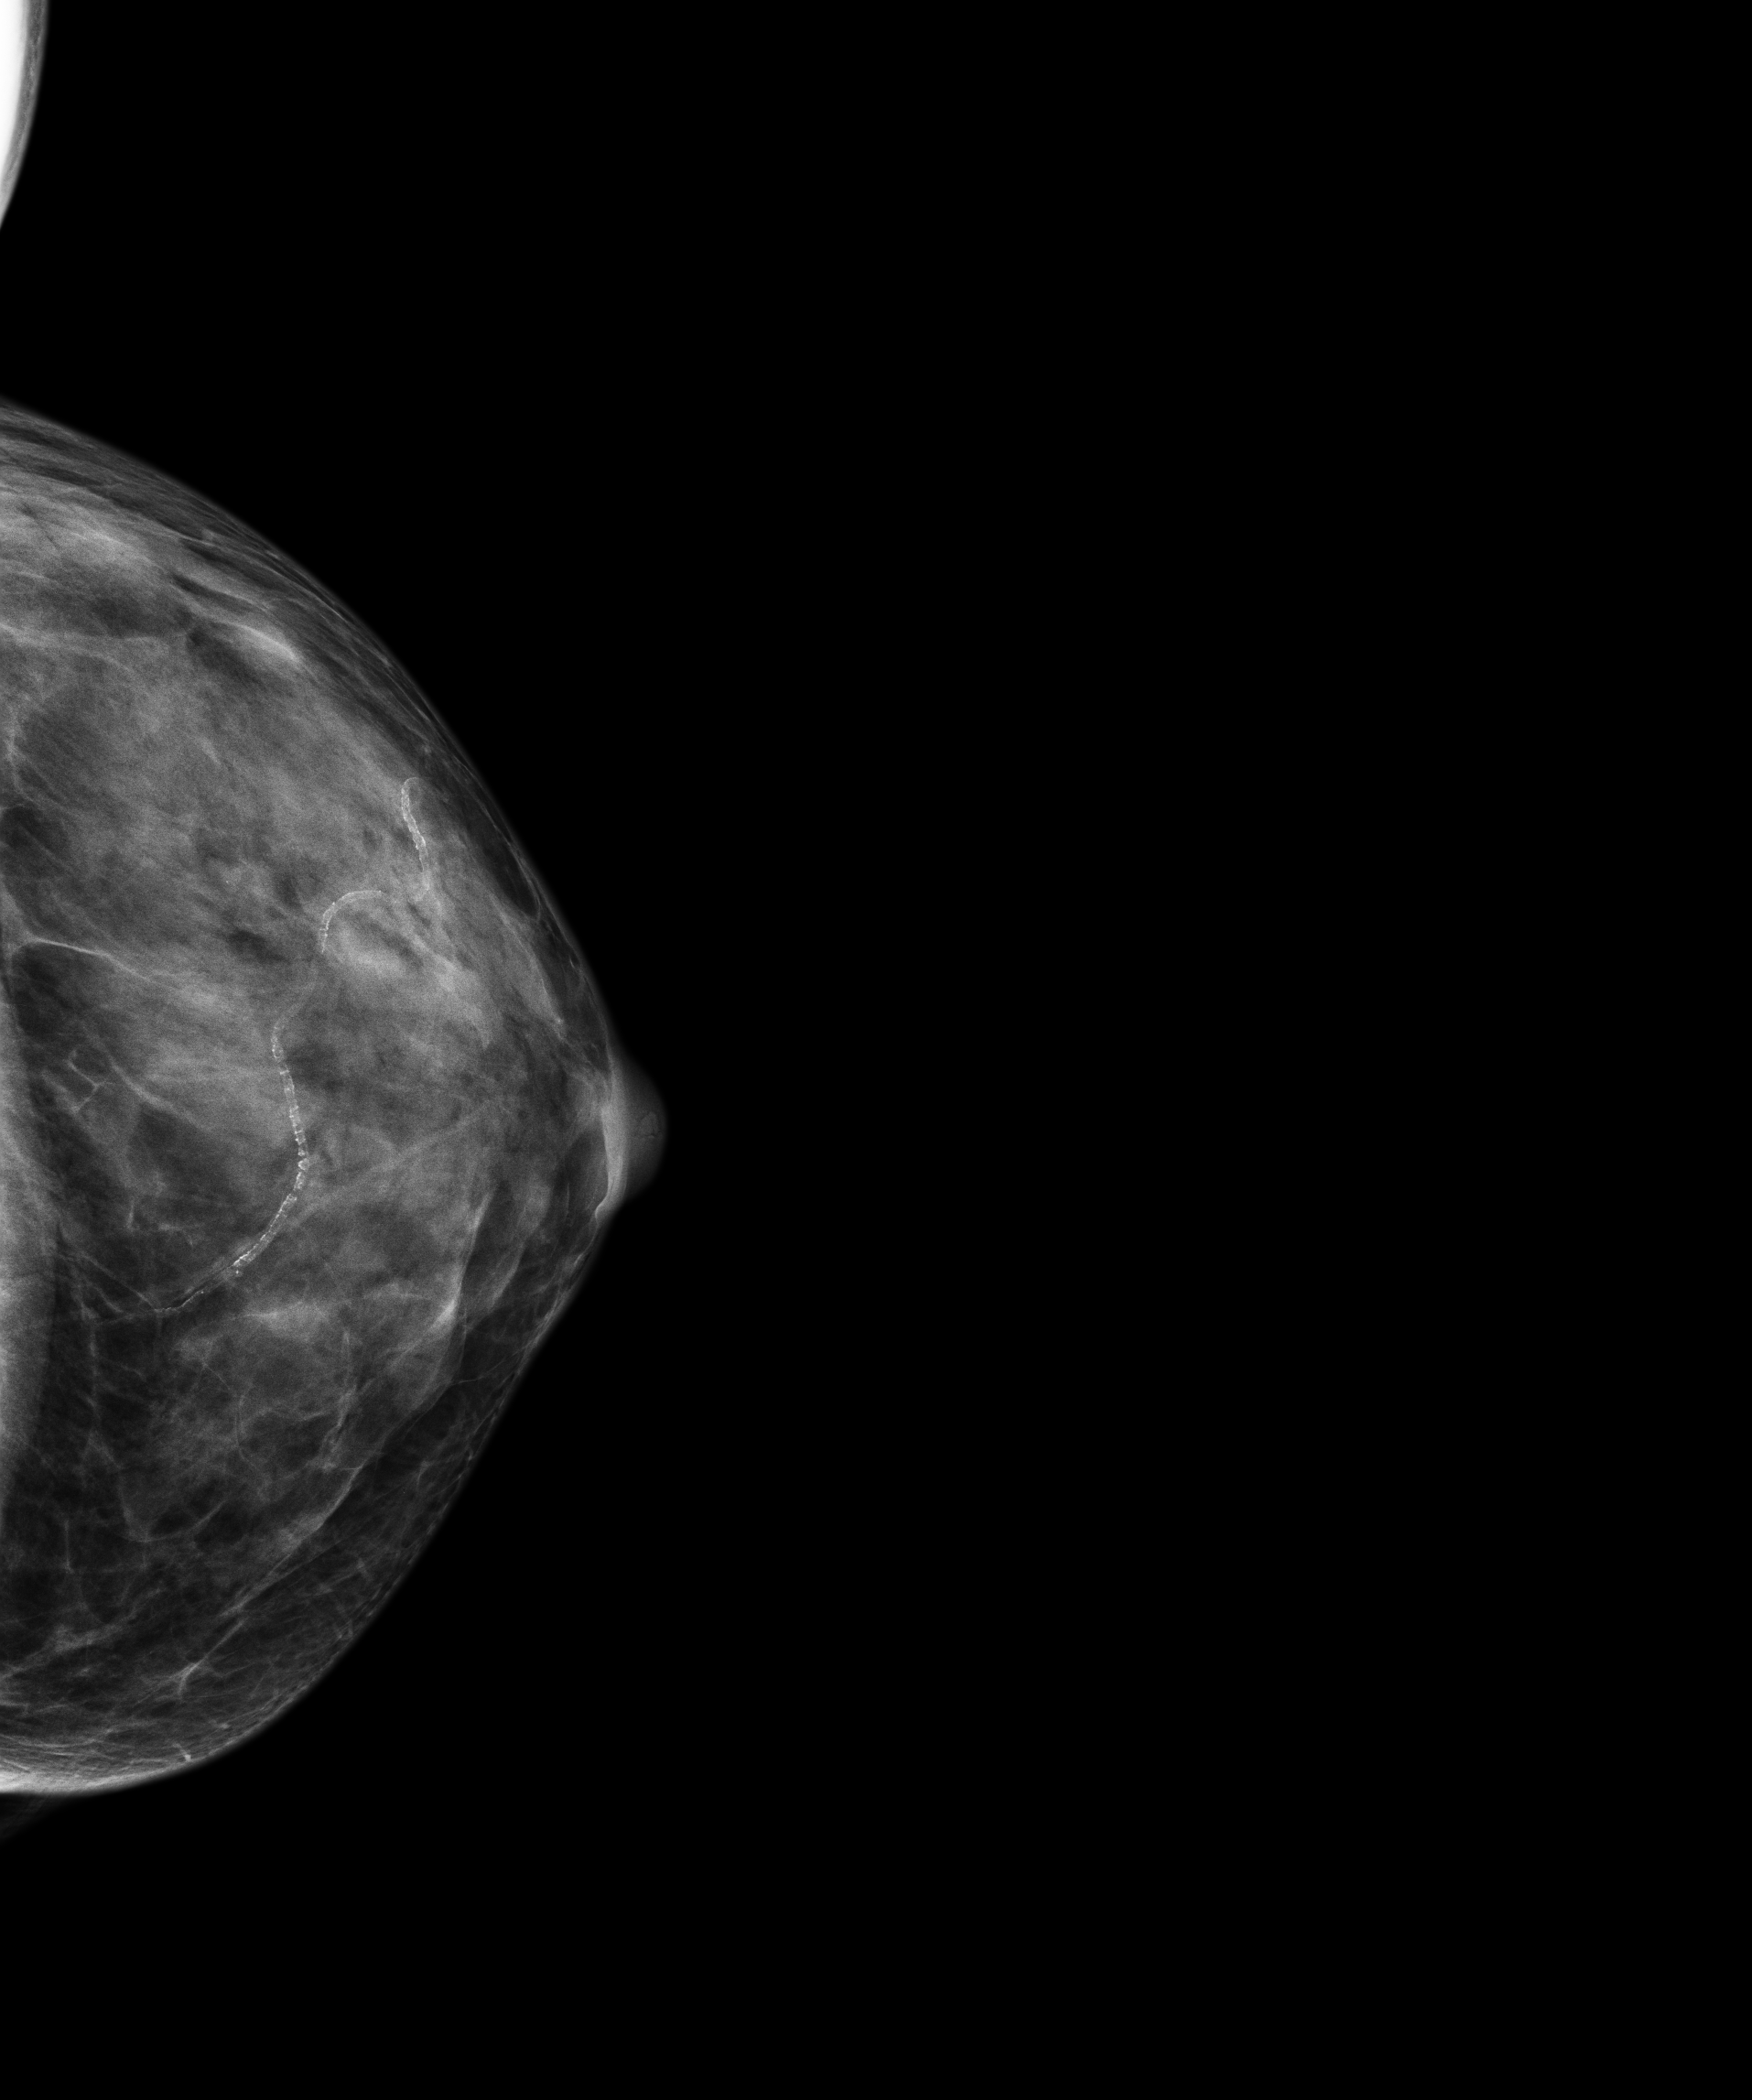
Annual screening mammography examination; compressed breast thickness 33 mm. Patient: female, 59 years.
Image type: full-field digital mammogram. Breast: left. Projection: craniocaudal (CC) view. BI-RADS breast density category at the screening exam (both breasts, scale 1–4): 4. Final BI-RADS assessment for this screening round (tomosynthesis exam, both breasts): category 1. Recall: no recall after this screen.